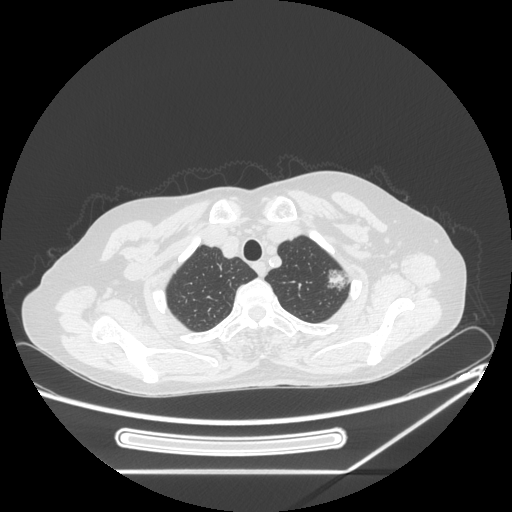
Chest CT, one axial slice. Position 211 of 250 along the scan axis. Reconstruction kernel STANDARD. Lung window (W 1500 / L -600 HU). 1.25 mm slice thickness. 512 × 512 image matrix, field of view 409 × 409 mm. Patient: female, 57 years. Case-level facts recorded for this patient, not image findings: clinical TNM (as recorded): T1c N0 M0.
Outlined on this slice (bounding box drawn by a radiologist):
- lung tumour (recorded histology: adenocarcinoma): bounding box [x1, y1, x2, y2] px = [323, 263, 348, 289]